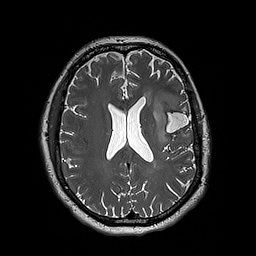
Brain MRI from a brain-tumour surgery series, one axial slice. Slice 86 of 192 in the series (ordered by position). 1 mm slice thickness. 256 × 256 image matrix, field of view 250 × 250 mm. From the clinical record (not read from this slice): histopathology: Astrocytoma; WHO grade: 3.
Structures marked on this image (expert manual segmentation):
- tumour: bounding box <153,92,180,144> (left, top, right, bottom; pixels)